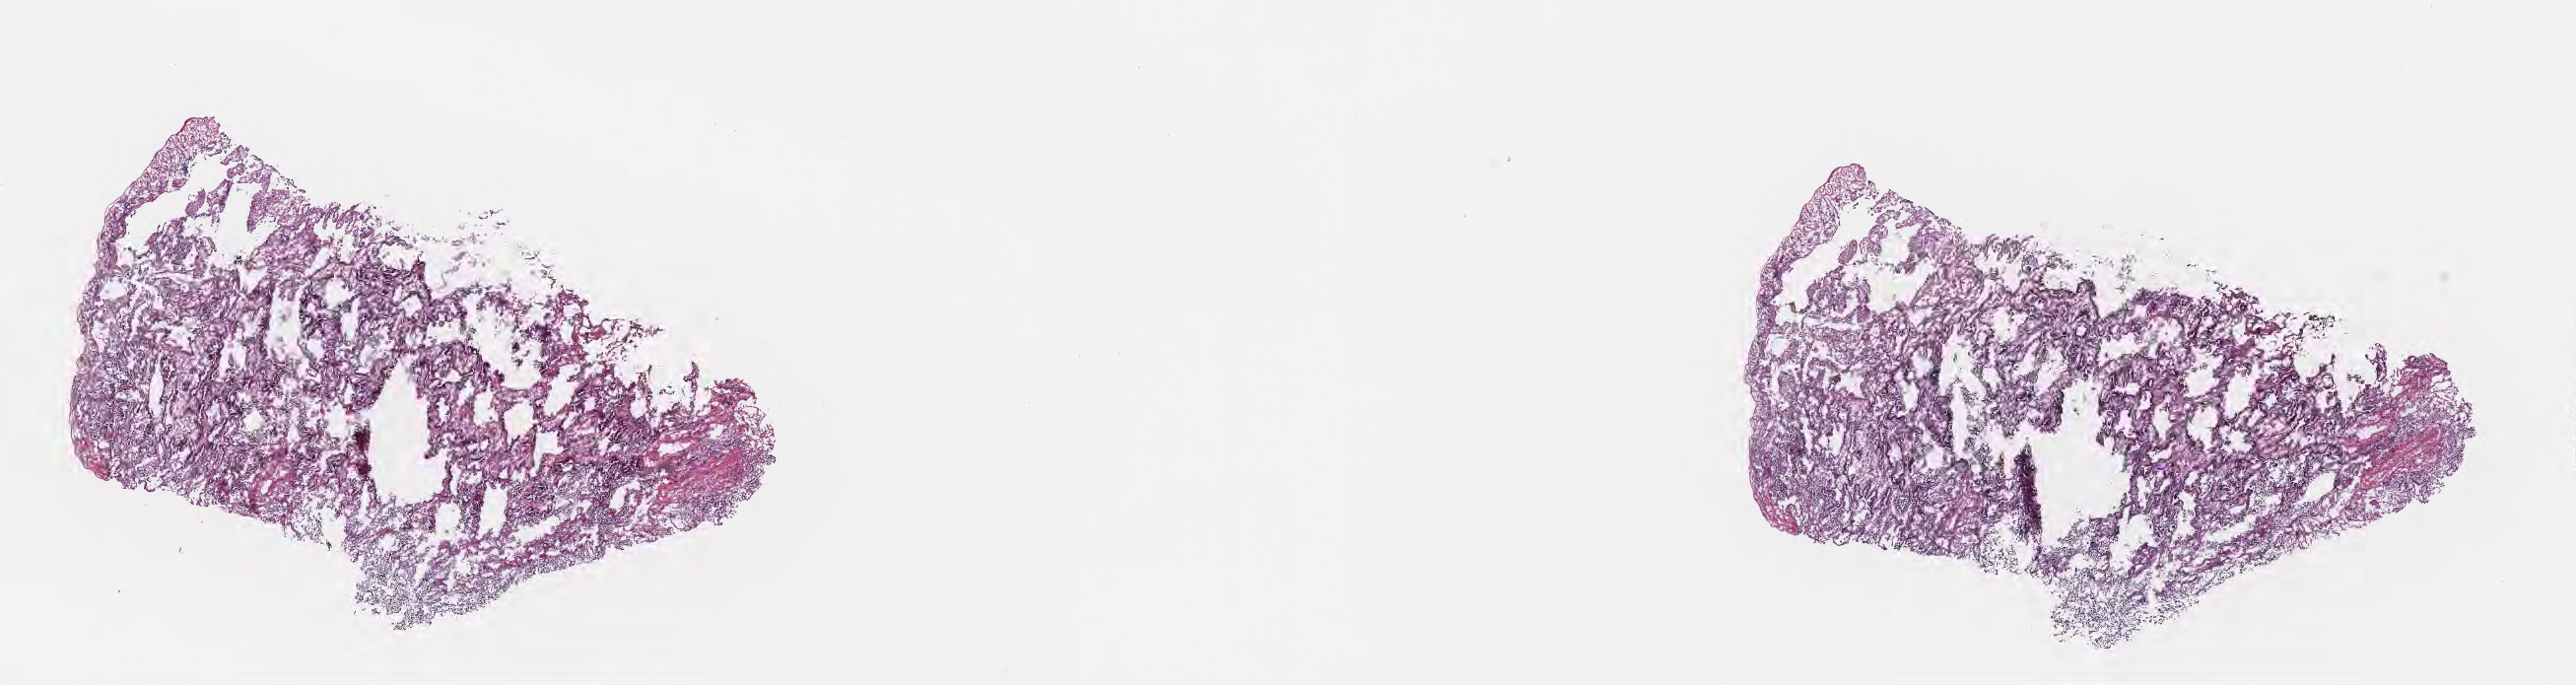
Digitized hematoxylin and eosin (H&E)-stained section — shown as a low-resolution overview of the whole scanned area (about 21.1 x 5.6 mm). Cryosection. Primary tumor. Site: lower lobe of left lung. Patient female; age 73 years. Slide review estimates, as recorded: tumor cells 85%, tumor nuclei 85%, stromal cells 13%, necrosis 1%, normal cells 1%. Infiltration values recorded for this section: lymphocyte infiltration 3%, monocyte infiltration 2%, neutrophil infiltration 4%.
Diagnosis: Adenocarcinoma, NOS. AJCC pathologic stage: Stage IA. Section: top of the tissue portion.